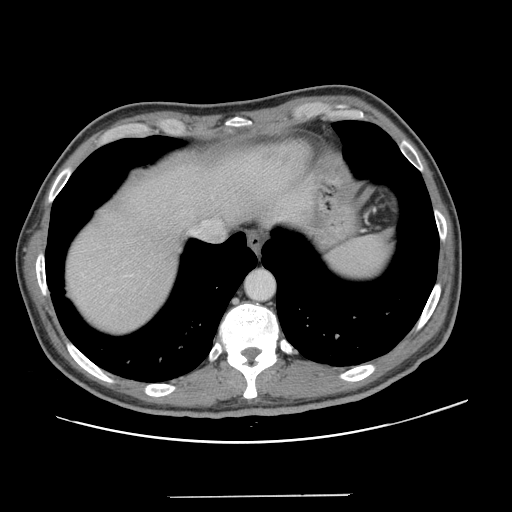
Contrast-enhanced abdominal CT, one axial slice; slice 115 of 131 in the series (ordered by position); 120 kVp; intravenous contrast given; soft-tissue window (W 400 / L 40 HU); 2.5 mm slice thickness; 512 × 512 image matrix, field of view 403 × 403 mm. Male patient, age 60 years. Case-level facts recorded for this patient, not image findings: diagnosis: colorectal cancer liver metastases, imaged before liver resection; multiple liver metastases: no.
Structures marked on this image (manually delineated by an expert):
- hepatic veins: bounding box [x1, y1, x2, y2] px = [190, 220, 216, 237]
- liver: [65, 143, 307, 336]
- planned liver remnant (the part of the liver to remain after resection): [65, 143, 307, 332]